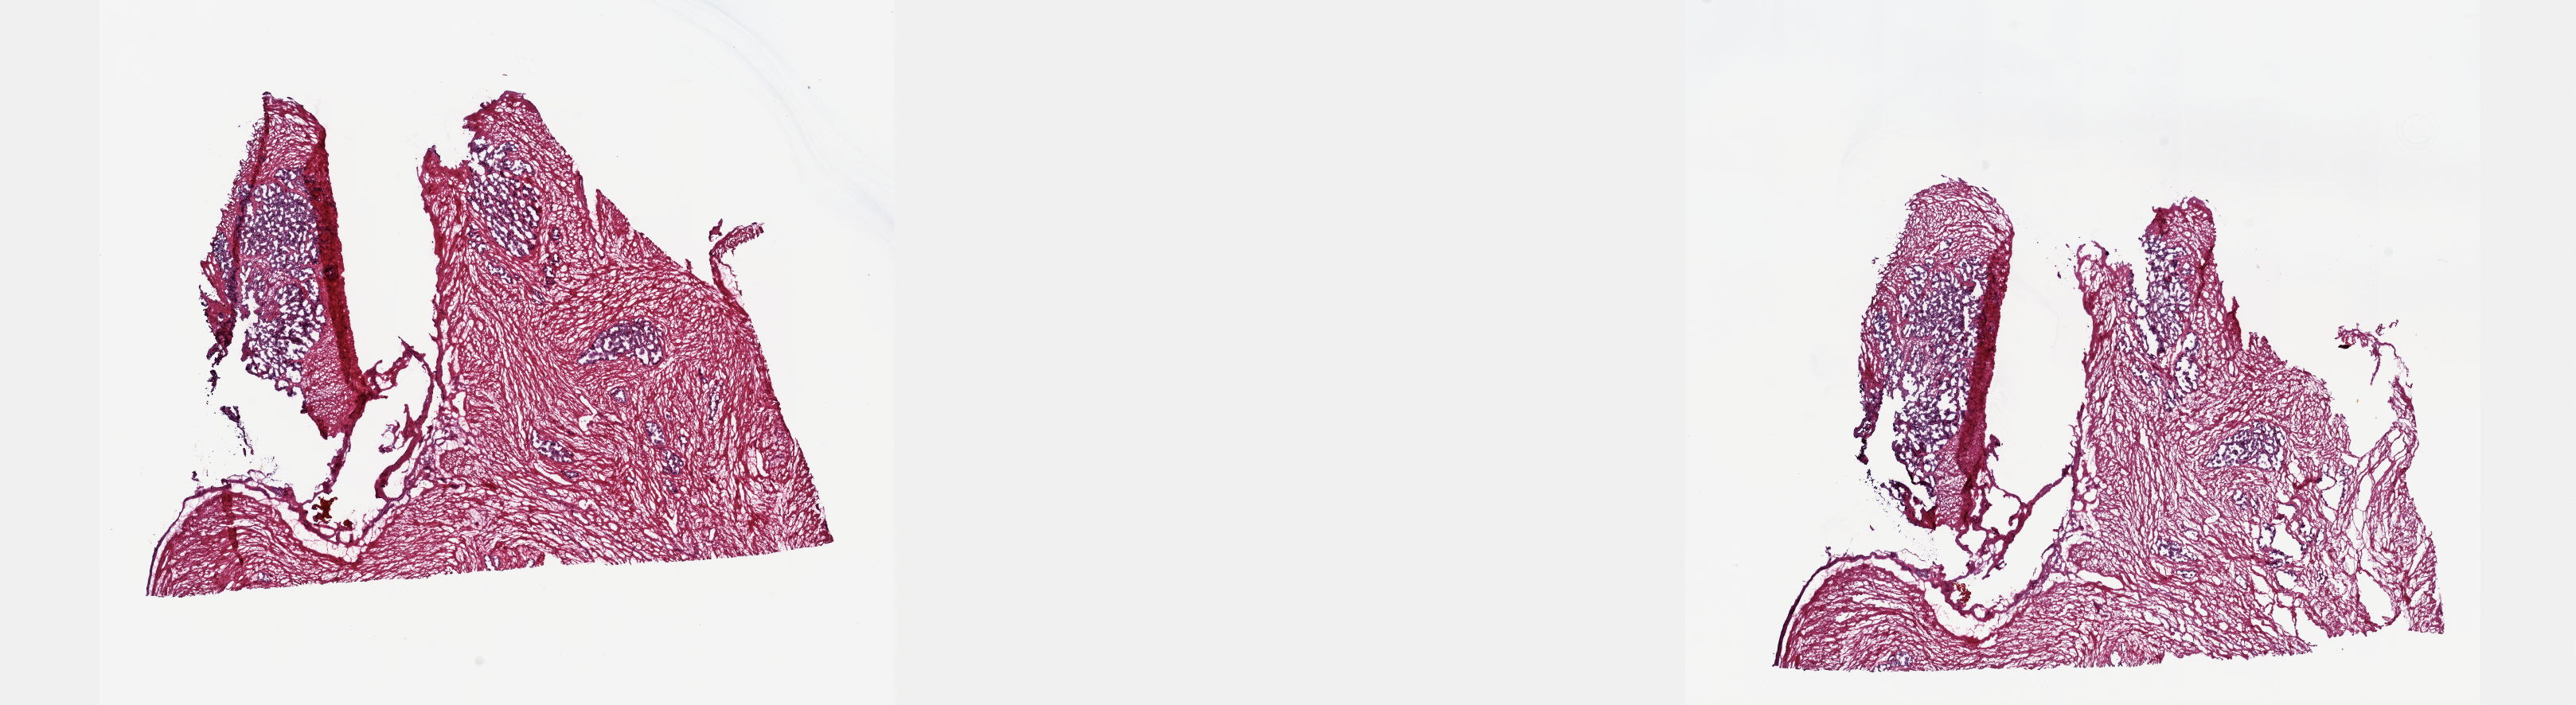
Hematoxylin and eosin (H&E) stained whole-slide image, shown as a low-resolution overview of the whole scanned area (about 26.1 x 7.1 mm). Frozen section from the top of the tissue portion. Solid tissue normal (non-tumour tissue) sample from the prostate. Male, age 55 years at initial diagnosis. Composition of this section per pathologist review: tumour cells 0%, tumour nuclei 0%, normal cells 100%, stromal cells 0%, necrosis 0%. Infiltration values recorded for this section: lymphocyte infiltration 1%, monocyte infiltration 0%, neutrophil infiltration 0%.
• this section: solid tissue normal sample (biorepository sample class)
• patient diagnosis: Adenocarcinoma, NOS (prostate gland)